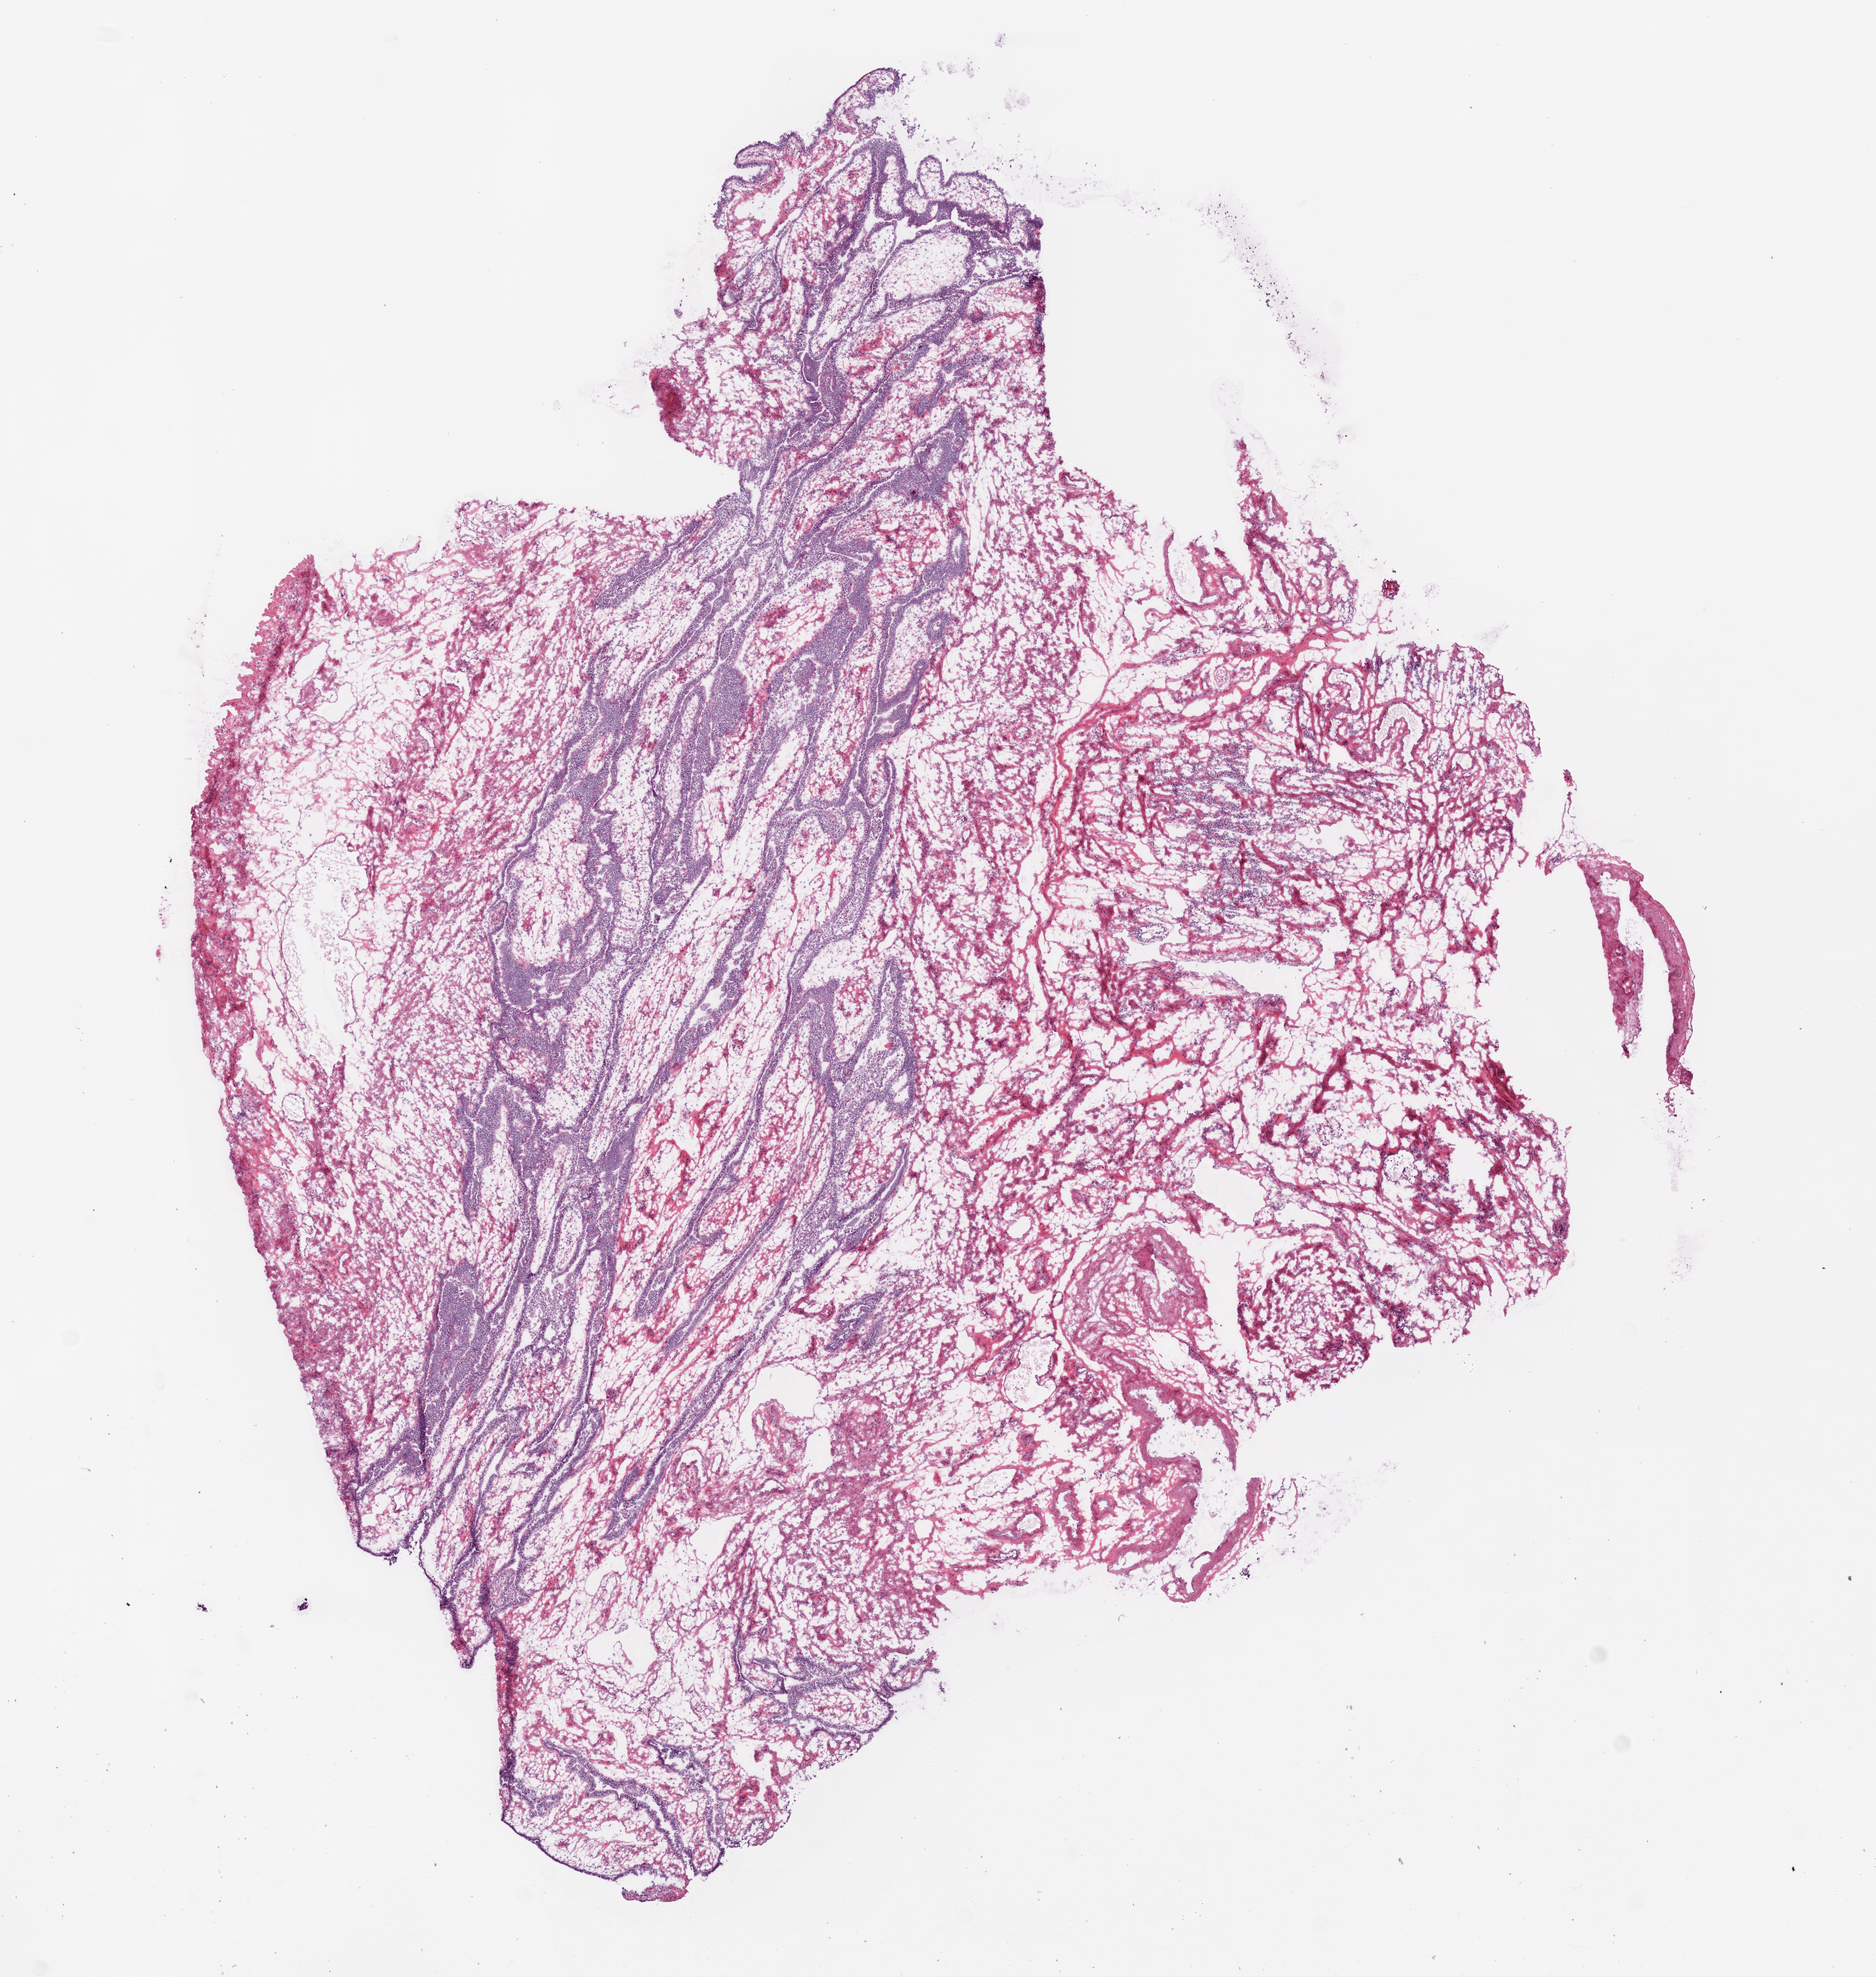
Digitized H&E tissue section (whole slide), a low-resolution overview of the entire scanned area, about 10.0 x 10.6 mm (from a 20x scan). Frozen section. Sample: solid tissue normal (non-tumour tissue), ovary. Female, age 55 years at initial diagnosis.
This section: solid tissue normal sample (biorepository sample class). Patient diagnosis: Serous cystadenocarcinoma, NOS.